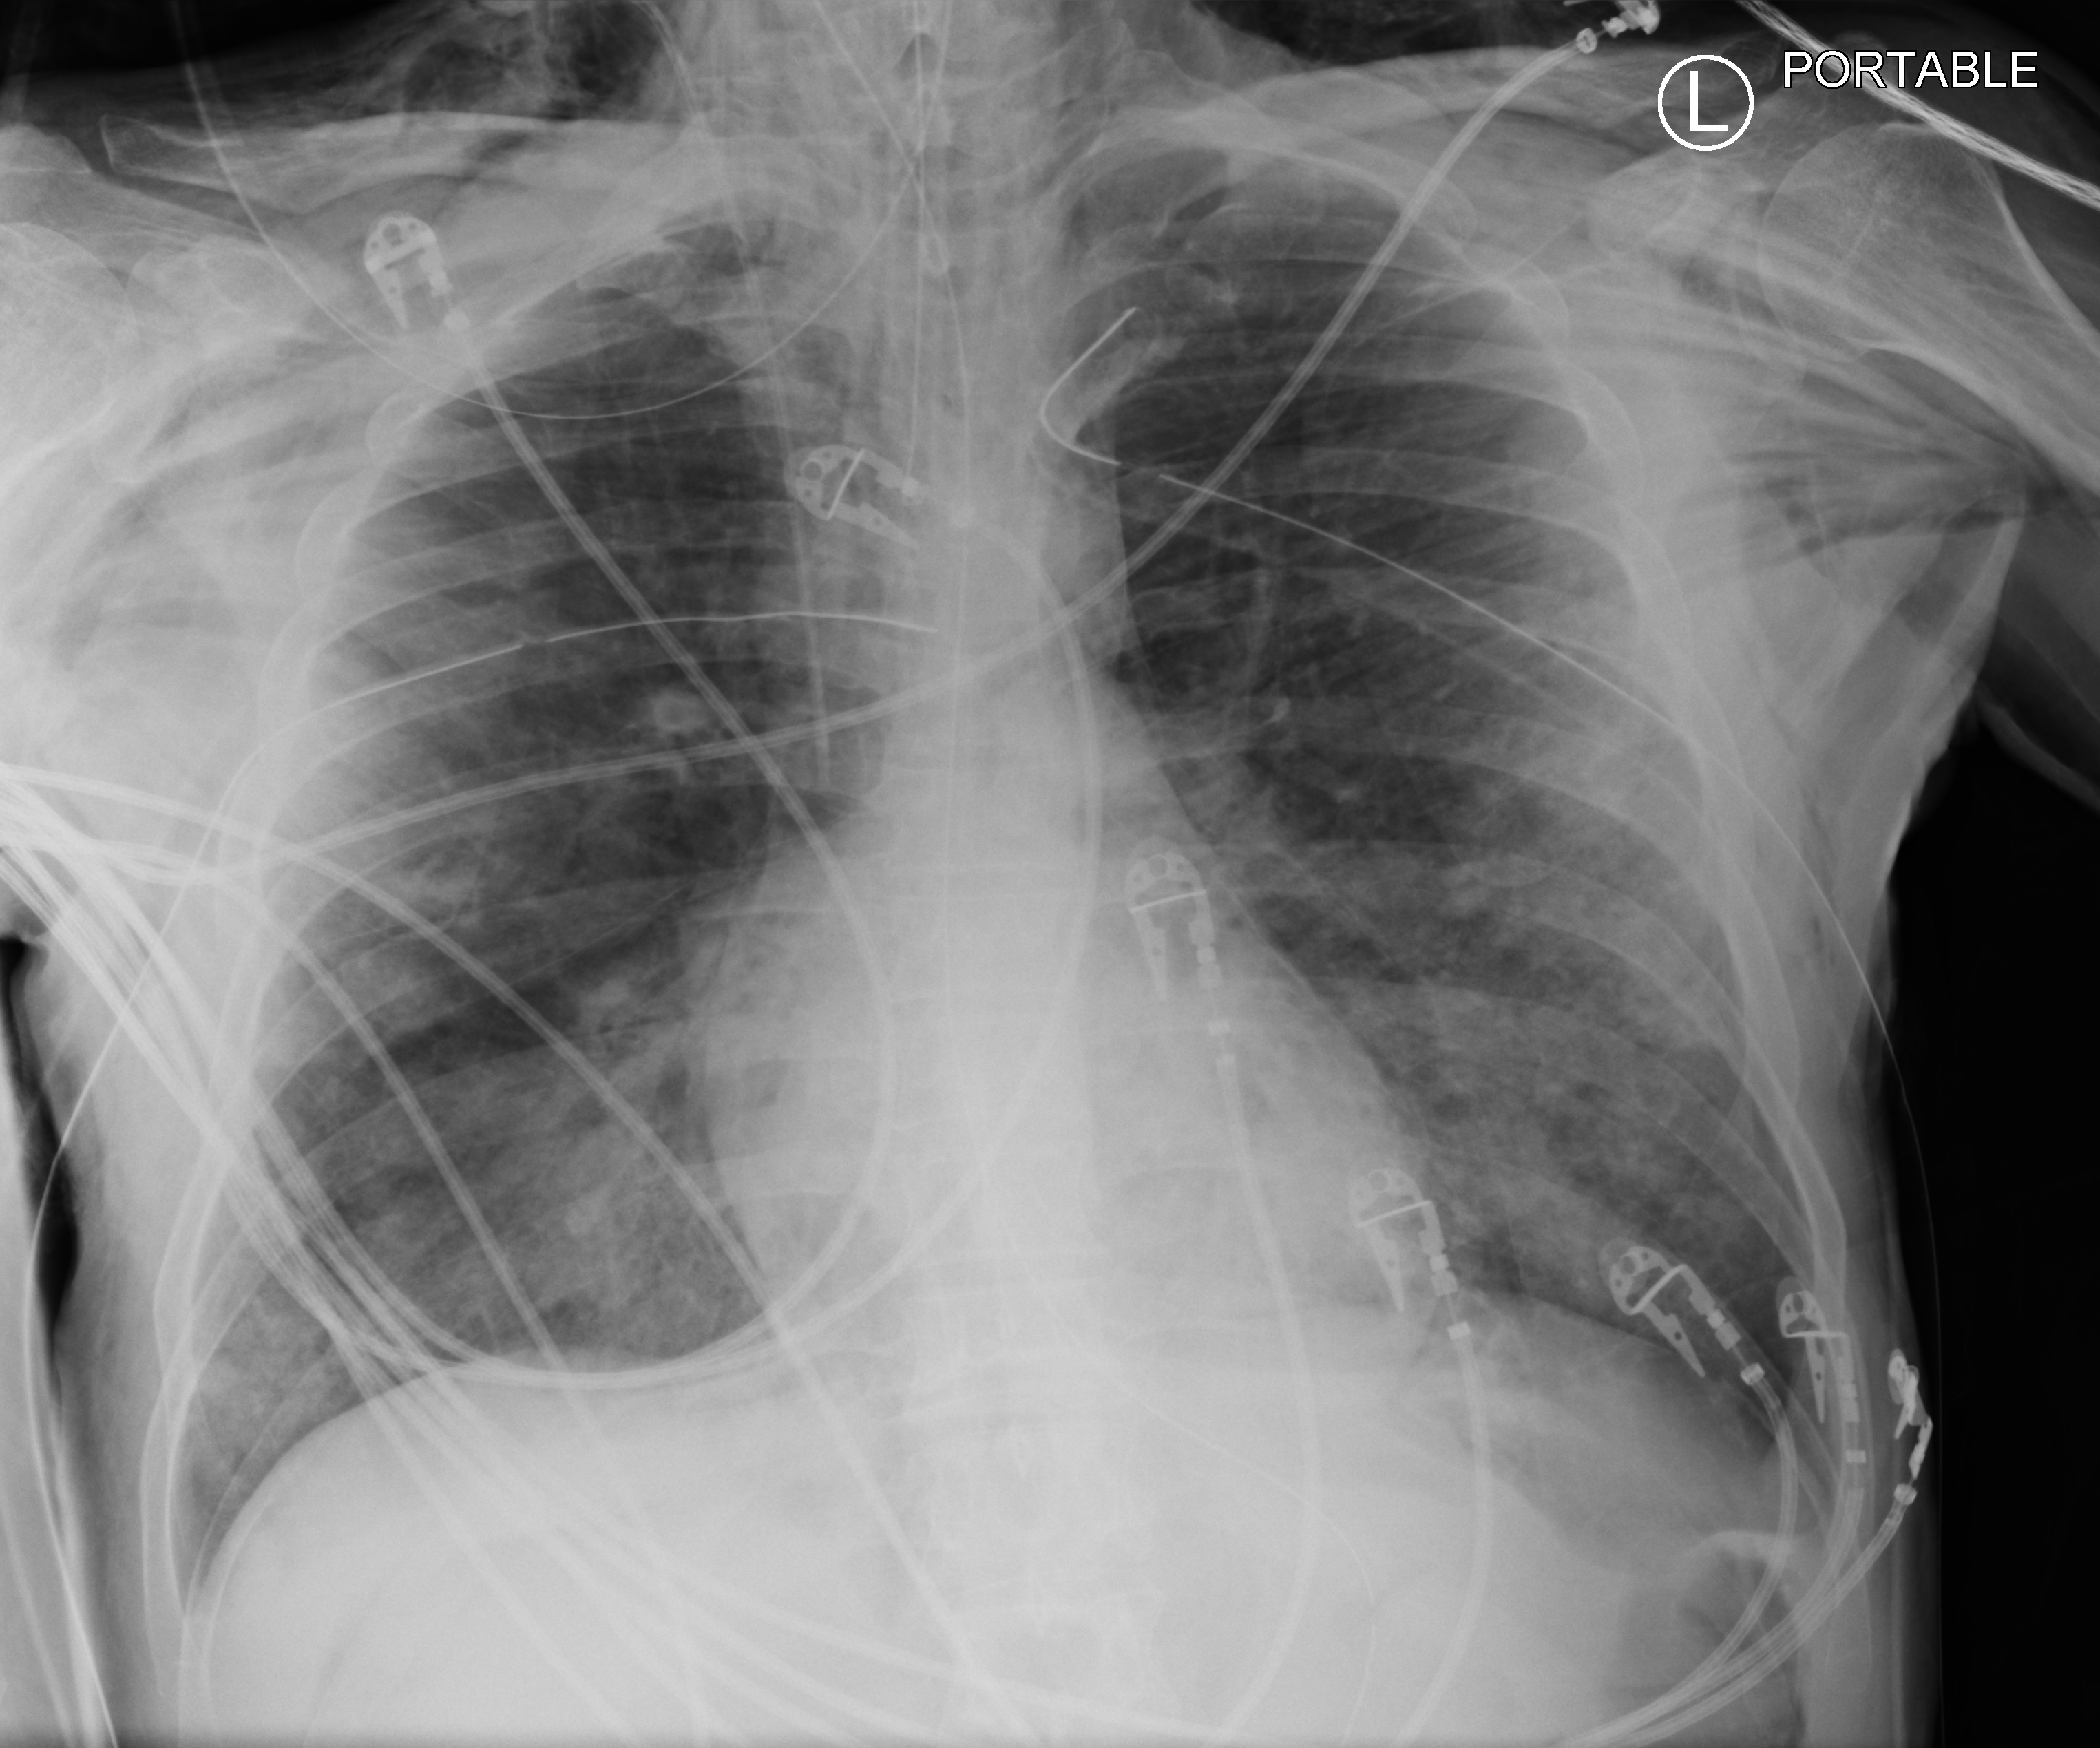
Bedside chest radiograph (computed radiography), anteroposterior (AP) projection. Male patient hospitalised with COVID-19, age 18–59 years.
From the hospital-stay record, not from the radiograph (when in the stay this image was taken is not recorded): admitted to intensive care during this hospital stay: yes; mechanically ventilated during this hospital stay: yes.